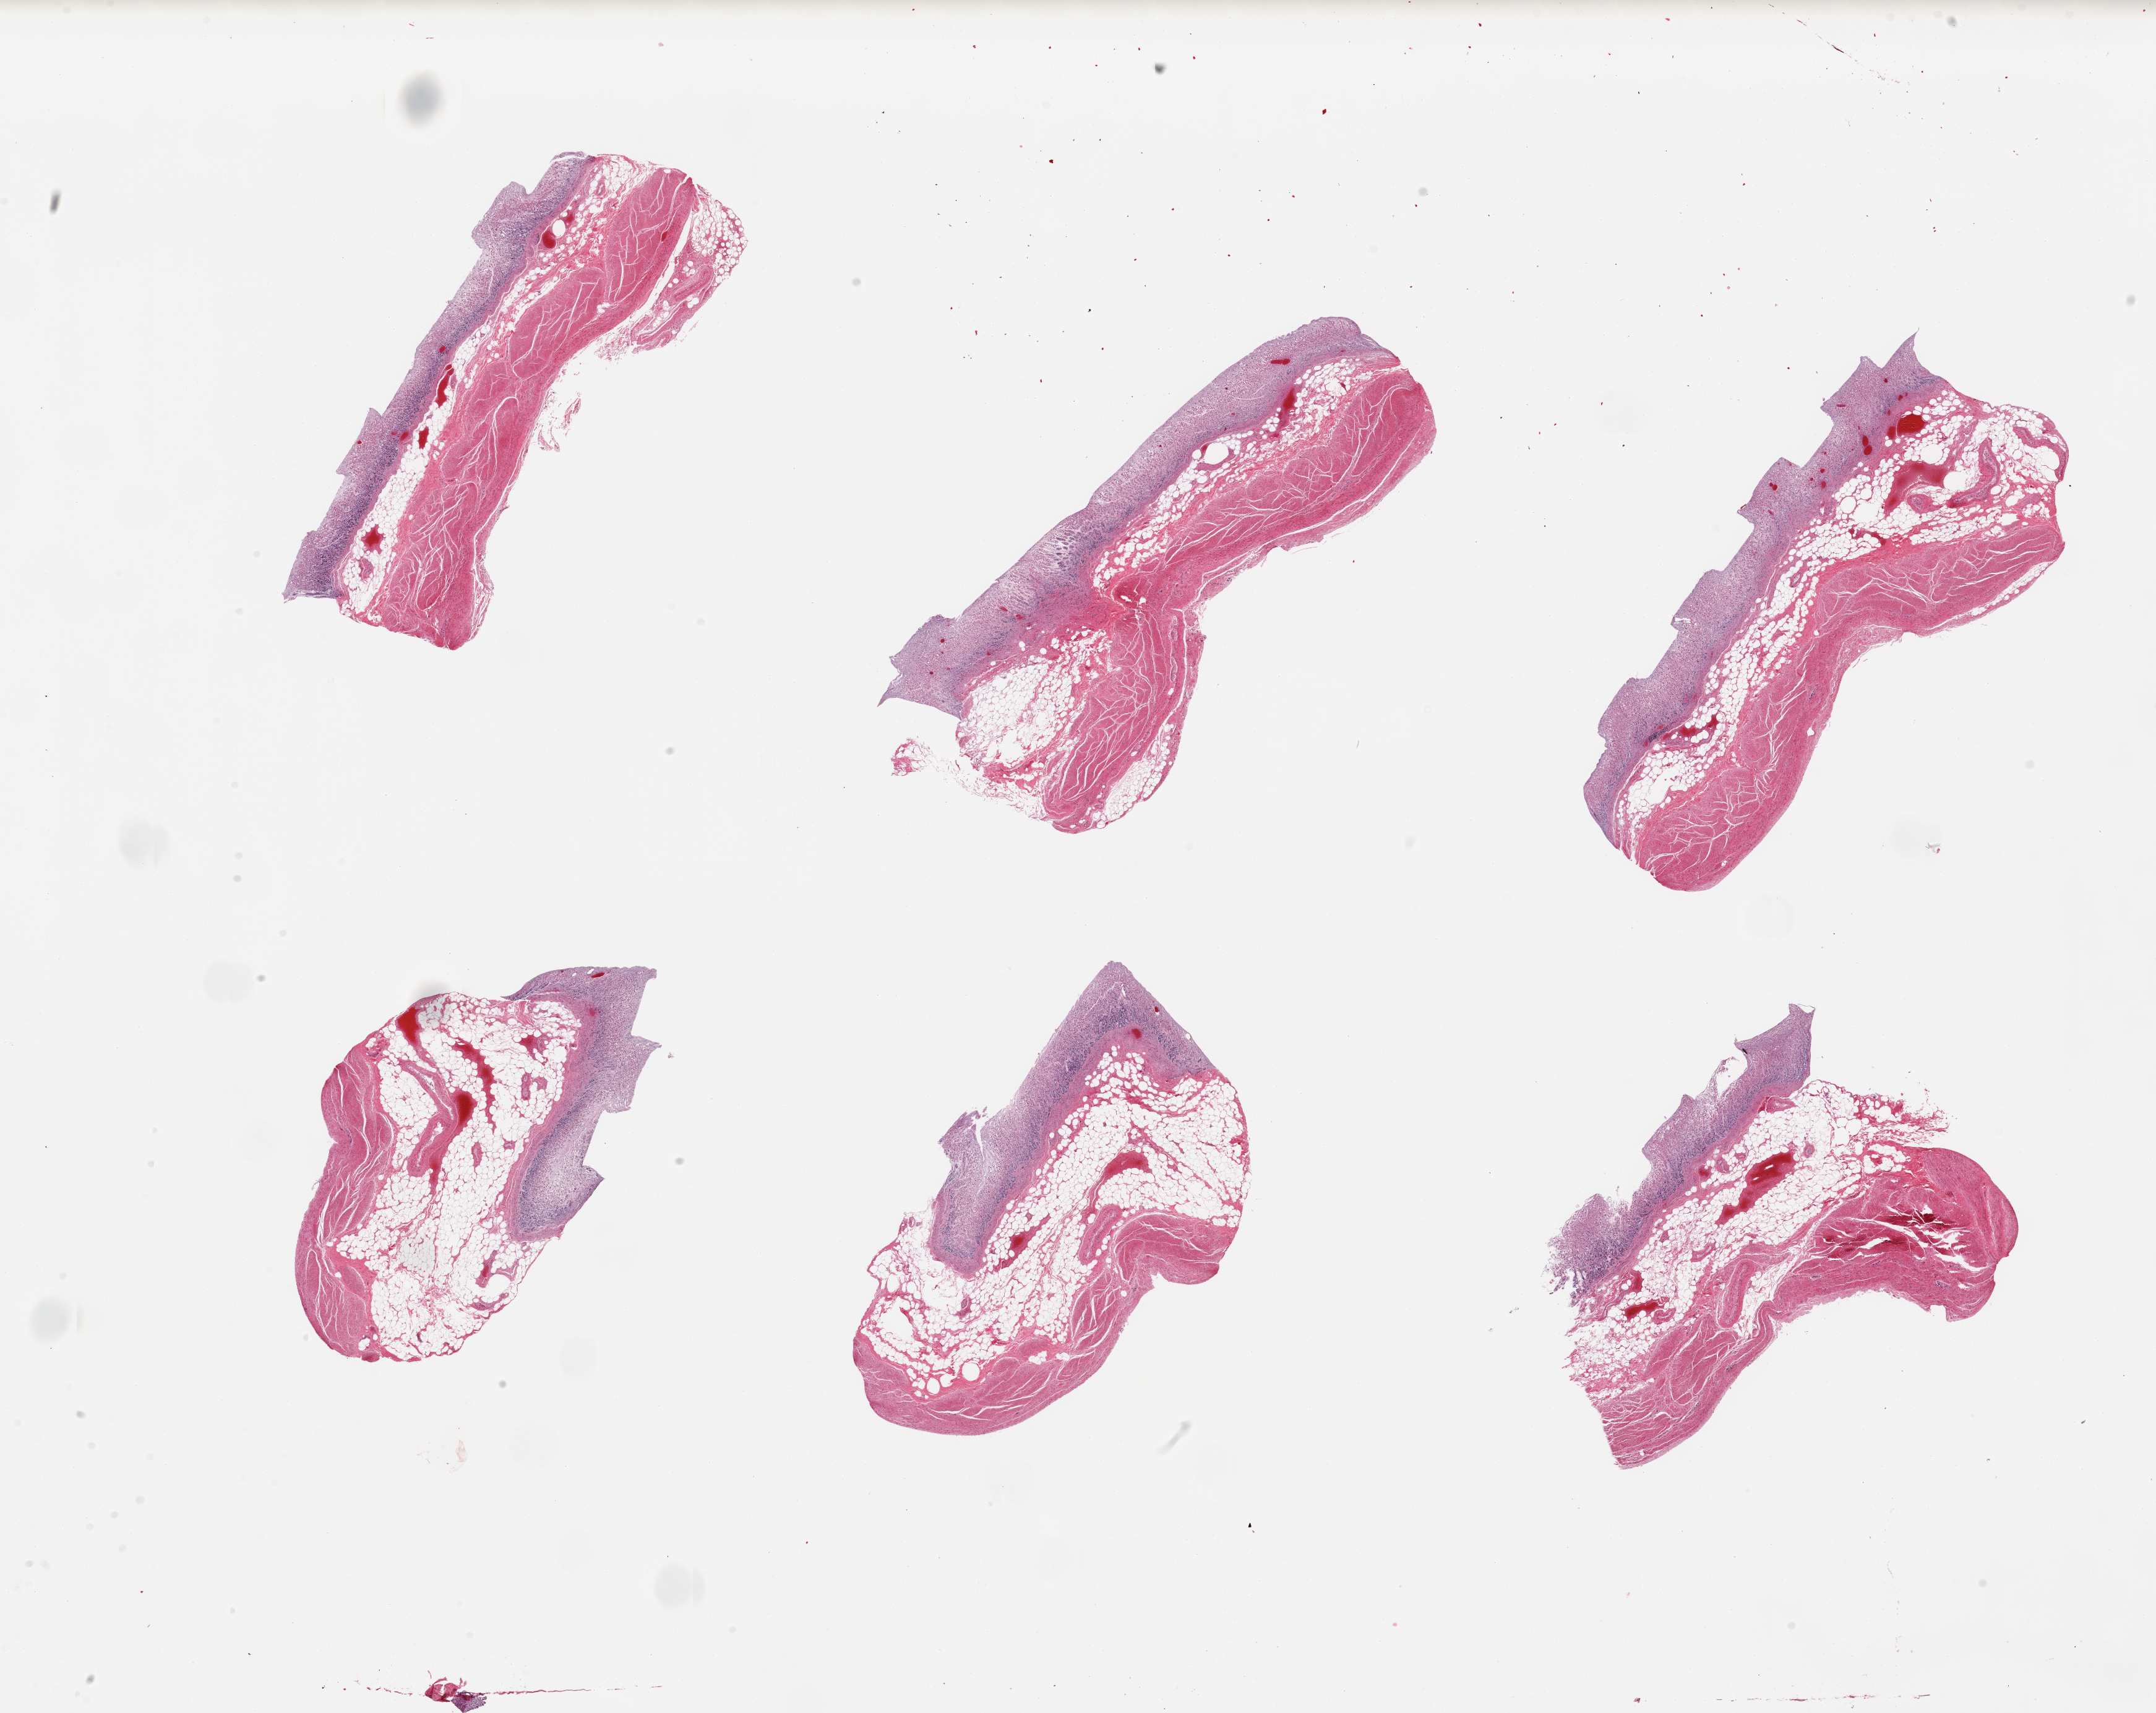
Whole-slide image, haematoxylin and eosin stain, brightfield, shown as a low-resolution overview of the whole scanned area (about 27.6 x 21.9 mm, slide scanned at 20x), PAXgene-fixed paraffin-embedded (PFPE) section, sampled site (target tissue): stomach, donor tissue sample. Donor sex: female.
Review note (as recorded): 6 pieces; full thickness sections, some up to 50% fat, mucosa is moderately to severely autolyzed.